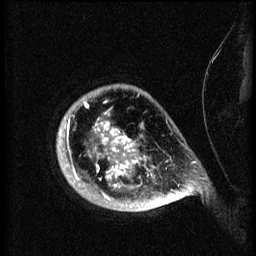
Breast MRI (dynamic contrast-enhanced), one sagittal slice; slice 58 of 60 in the series (ordered by position); 3 images stored at this slice position (order not interpretable as contrast timing); 1.5 T; TE 4.2 ms, TR 8.2 ms; 256 × 256 image matrix, field of view 200 × 200 mm. Patient: female, 50 years.
Annotated regions visible in this slice (semi-automatic segmentation, software-assisted and operator-edited):
- analysis volume of interest (the breast-tissue region the enhancement analysis was run in; not a lesion): box from (x=58, y=86) to (x=173, y=213) px
- tumour enhancement mask (voxels above the 70 % enhancement threshold inside the analysis volume of interest): (x=60, y=102)–(x=173, y=205)